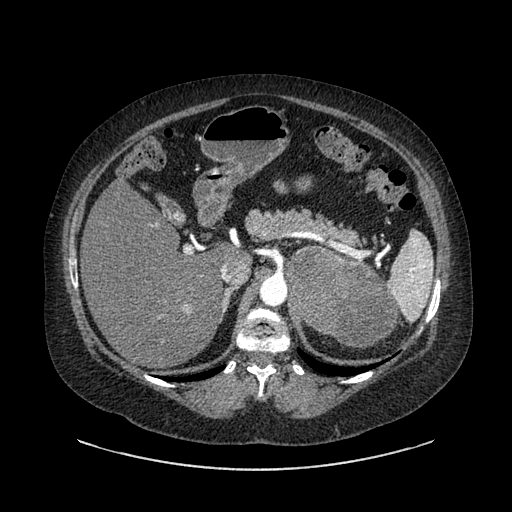
Contrast-enhanced abdominal CT, one axial slice; slice 590 of 769 in the series (ordered by position); reconstruction kernel SOFT; soft-tissue window (W 400 / L 40 HU); 0.62 mm slice thickness; 512 × 512 image matrix, field of view 460 × 460 mm. Patient: female, 61 years. From the clinical record (not read from this slice): diagnosis: adrenocortical carcinoma; tumour side: left adrenal; tumour size at pathology: 13 cm; Ki-67 index: 79 %; stage (as recorded): 2.
Outlined on this slice (semi-automatically segmented with operator editing):
- mass: bounding box (x1, y1, x2, y2) in pixels: (288, 248, 395, 346)